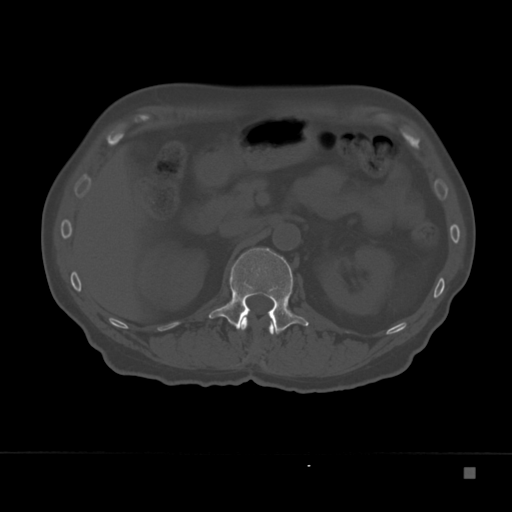
CT including the spine, one axial slice. Slice 115 of 332 in the series (ordered by position). 120 kVp. Bone window (W 1800 / L 400 HU). 1.5 mm slice thickness. 512 × 512 image matrix, field of view 389 × 389 mm. Patient: male, 72 years. From the clinical record (not read from this slice): primary cancer: skeletal.
Structures marked on this image (semi-automatic segmentation, software-assisted and operator-edited):
- L1 vertebra: bounding box (x1, y1, x2, y2) in pixels: (209, 248, 309, 334)
- T12 vertebra: (241, 317, 274, 335)